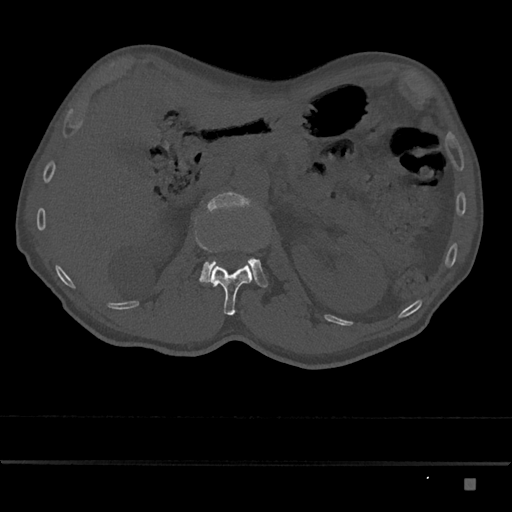
CT including the spine, one axial slice; reconstruction kernel Br40s/3; bone window (W 1800 / L 400 HU); 0.5 mm slice thickness; 512 × 512 image matrix. Patient: male, 72 years. Case-level facts recorded for this patient, not image findings: primary cancer: prostate.
Annotated regions visible in this slice (semi-automatic segmentation, software-assisted and operator-edited):
- L1 vertebra: bounding box <208,263,253,315> (left, top, right, bottom; pixels)
- L2 vertebra: <199,192,268,287>